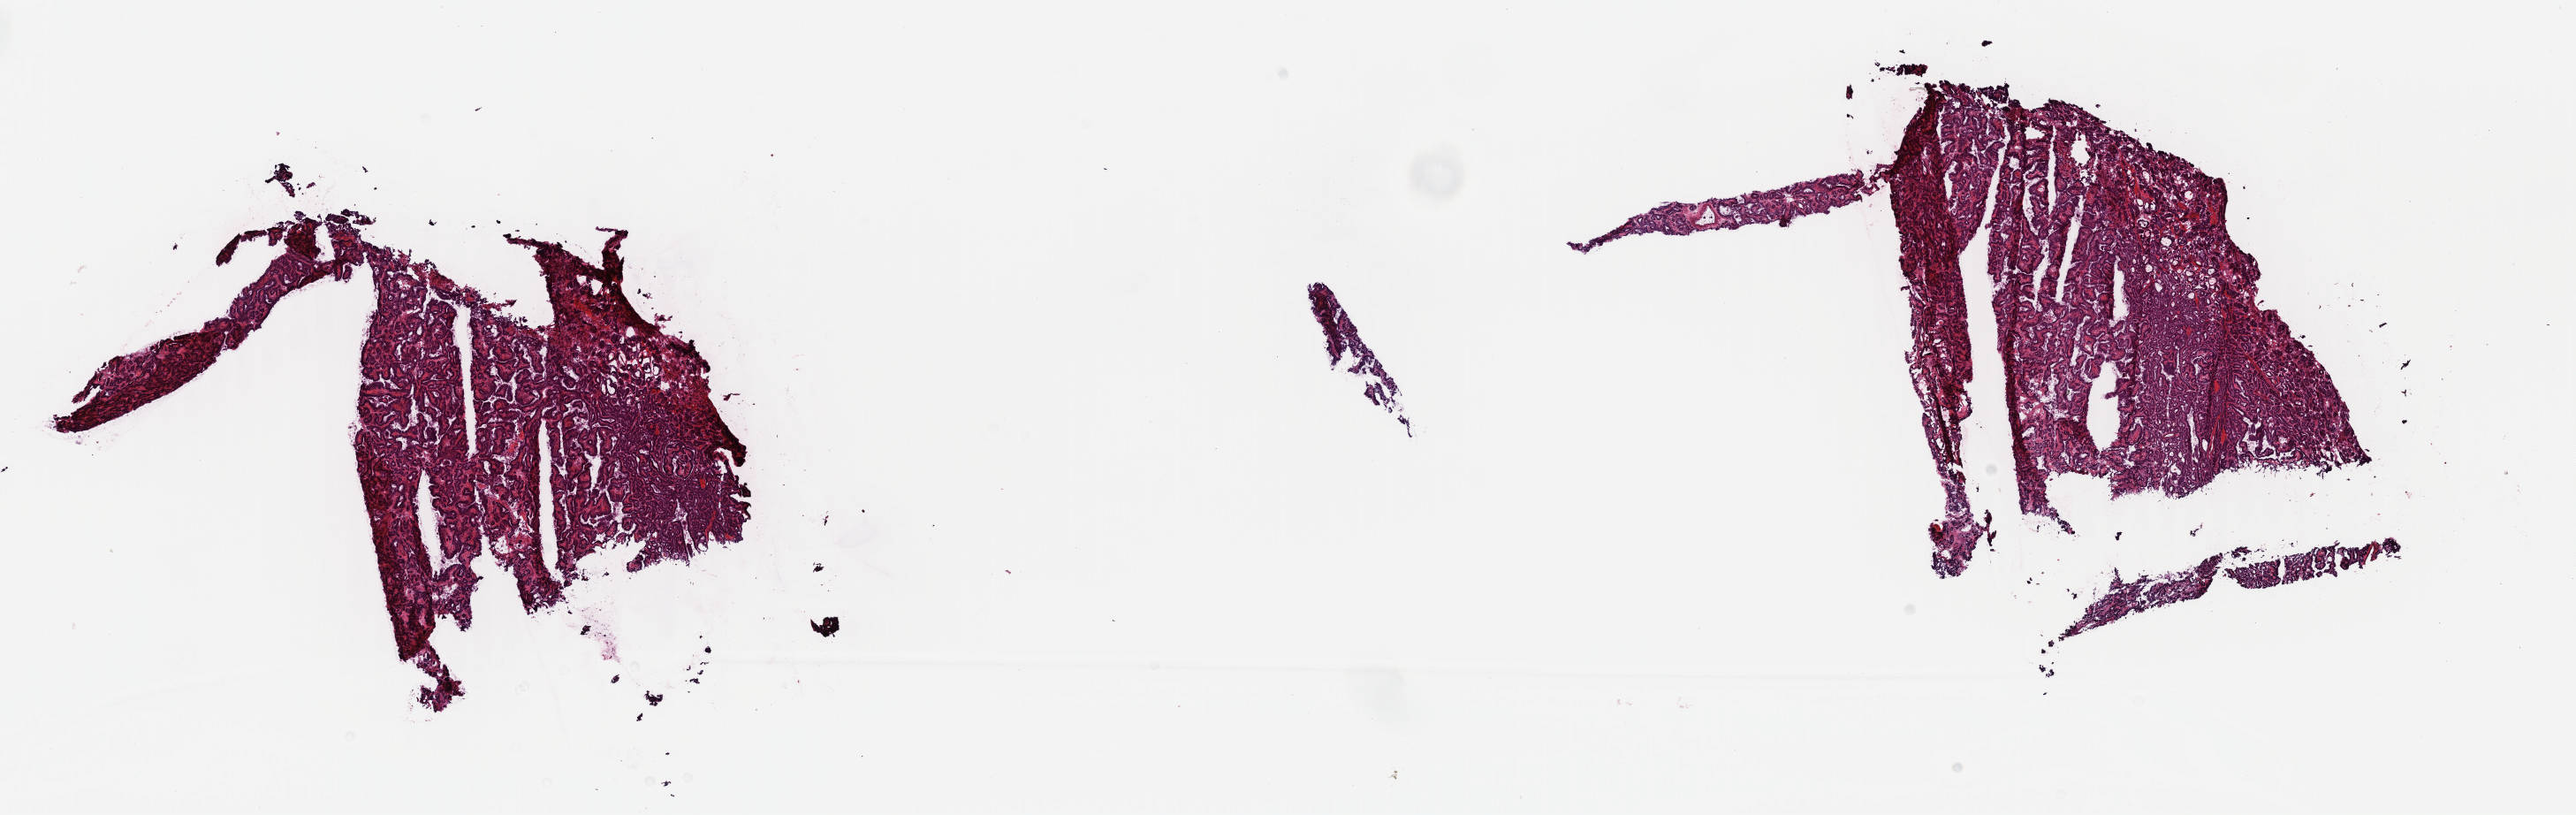
Whole-slide histology image, H&E-stained, low-resolution overview of the scanned area, about 23.0 x 7.3 mm; frozen section; thyroid, primary tumour sample. Female, age 42 years at initial diagnosis. Slide review estimates, as recorded: tumour cells 90%, tumour nuclei 90%, normal cells 0%, stromal cells 10%, necrosis 0%. Infiltration values recorded for this section: lymphocyte infiltration 1%, monocyte infiltration 1%, neutrophil infiltration 0%.
• TNM: T1b N0 M0
• AJCC pathologic stage: I (7th edition)
• diagnosis: Papillary adenocarcinoma, NOS (thyroid gland)
• laterality: bilateral